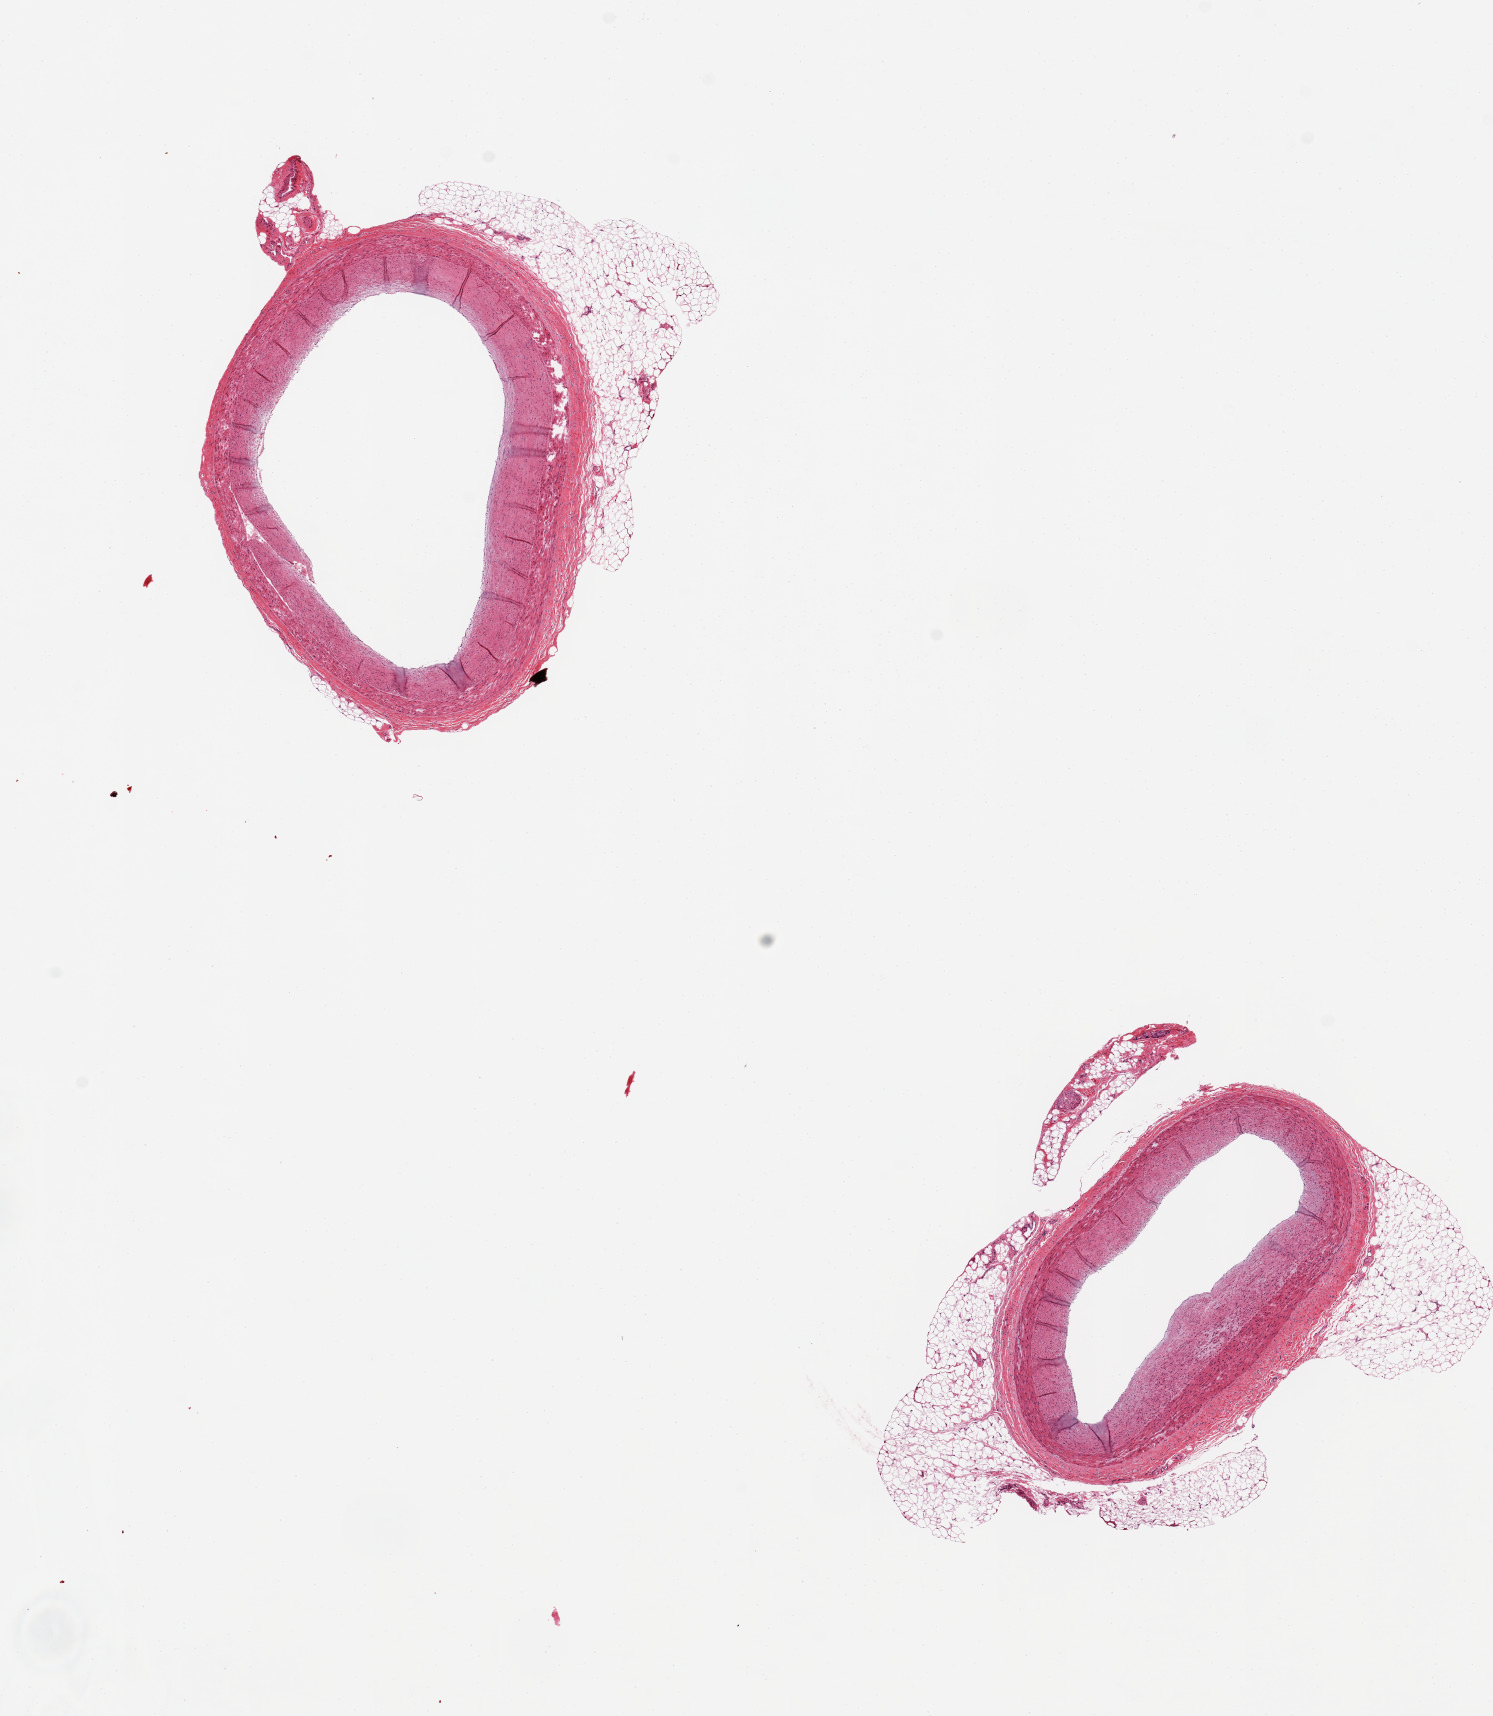
H&E whole-slide image — shown as a low-resolution overview of the whole scanned area (about 11.8 x 13.6 mm), PAXgene-fixed paraffin-embedded (PFPE) section, section of coronary artery (target tissue), tissue donor sample. Female donor.
Review note (as recorded): 2 pieces 4 mm arteries with virtually no sclerosis; ~20% adherent adipose.